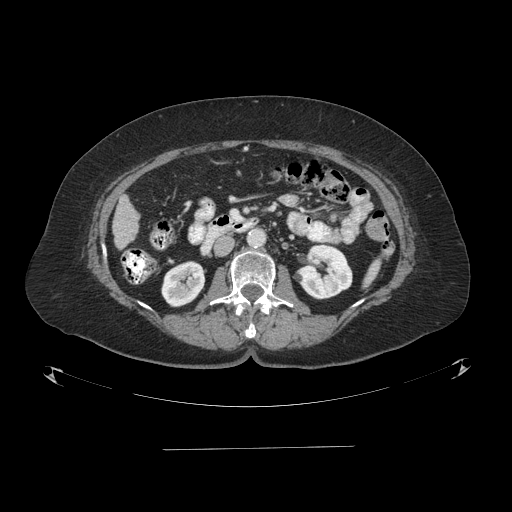
Contrast-enhanced abdominal CT (liver protocol), one axial slice; slice 21 of 103 in the series (ordered by position); 120 kVp; one of 2 acquisitions stored at this slice position; soft-tissue window (W 400 / L 40 HU); 2.5 mm slice thickness; 512 × 512 image matrix, field of view 500 × 500 mm. Case-level facts recorded for this patient, not image findings: diagnosis: hepatocellular carcinoma (patient treated with transarterial chemoembolisation; whether this scan precedes or follows treatment is not stated here); TNM stage (as recorded): Stage-IIIA.
Annotated regions visible in this slice (semi-automatic segmentation, software-assisted and operator-edited):
- liver parenchyma outside the tumour (the mass and vessels are separate outlines, so this box may not span the whole liver): bounding box [x1, y1, x2, y2] px = [112, 194, 138, 250]